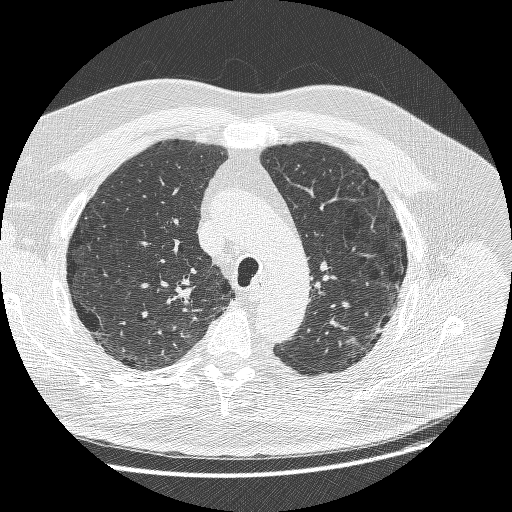
Chest CT (low-dose screening protocol), one axial image. Baseline screening round. Lung window (W 1500 / L -600 HU). 1.25 mm slice thickness. 120 kVp. Slice 194 of 258 in the series. Male participant, aged 68 years at enrolment.
- Expert reader's lesion annotation, bounding box [x1, y1, x2, y2] px = [335, 306, 391, 362].
- Reader record for this screening exam (exam-level; its link to the box is not recorded): non-calcified nodule or mass ≥4 mm, left upper lobe, 15 × 14 mm, smooth margins, soft tissue attenuation.
- Official screen result: positive, change unspecified: nodule(s) >= 4 mm or enlarging nodule(s), mass(es), or other non-specific abnormalities suspicious for lung cancer.
- Lung cancer was diagnosed 19 days after this screen: adenosquamous carcinoma, left upper lobe, poorly differentiated (G3), stage IIIB (AJCC 6th edition), 32 mm at pathology.